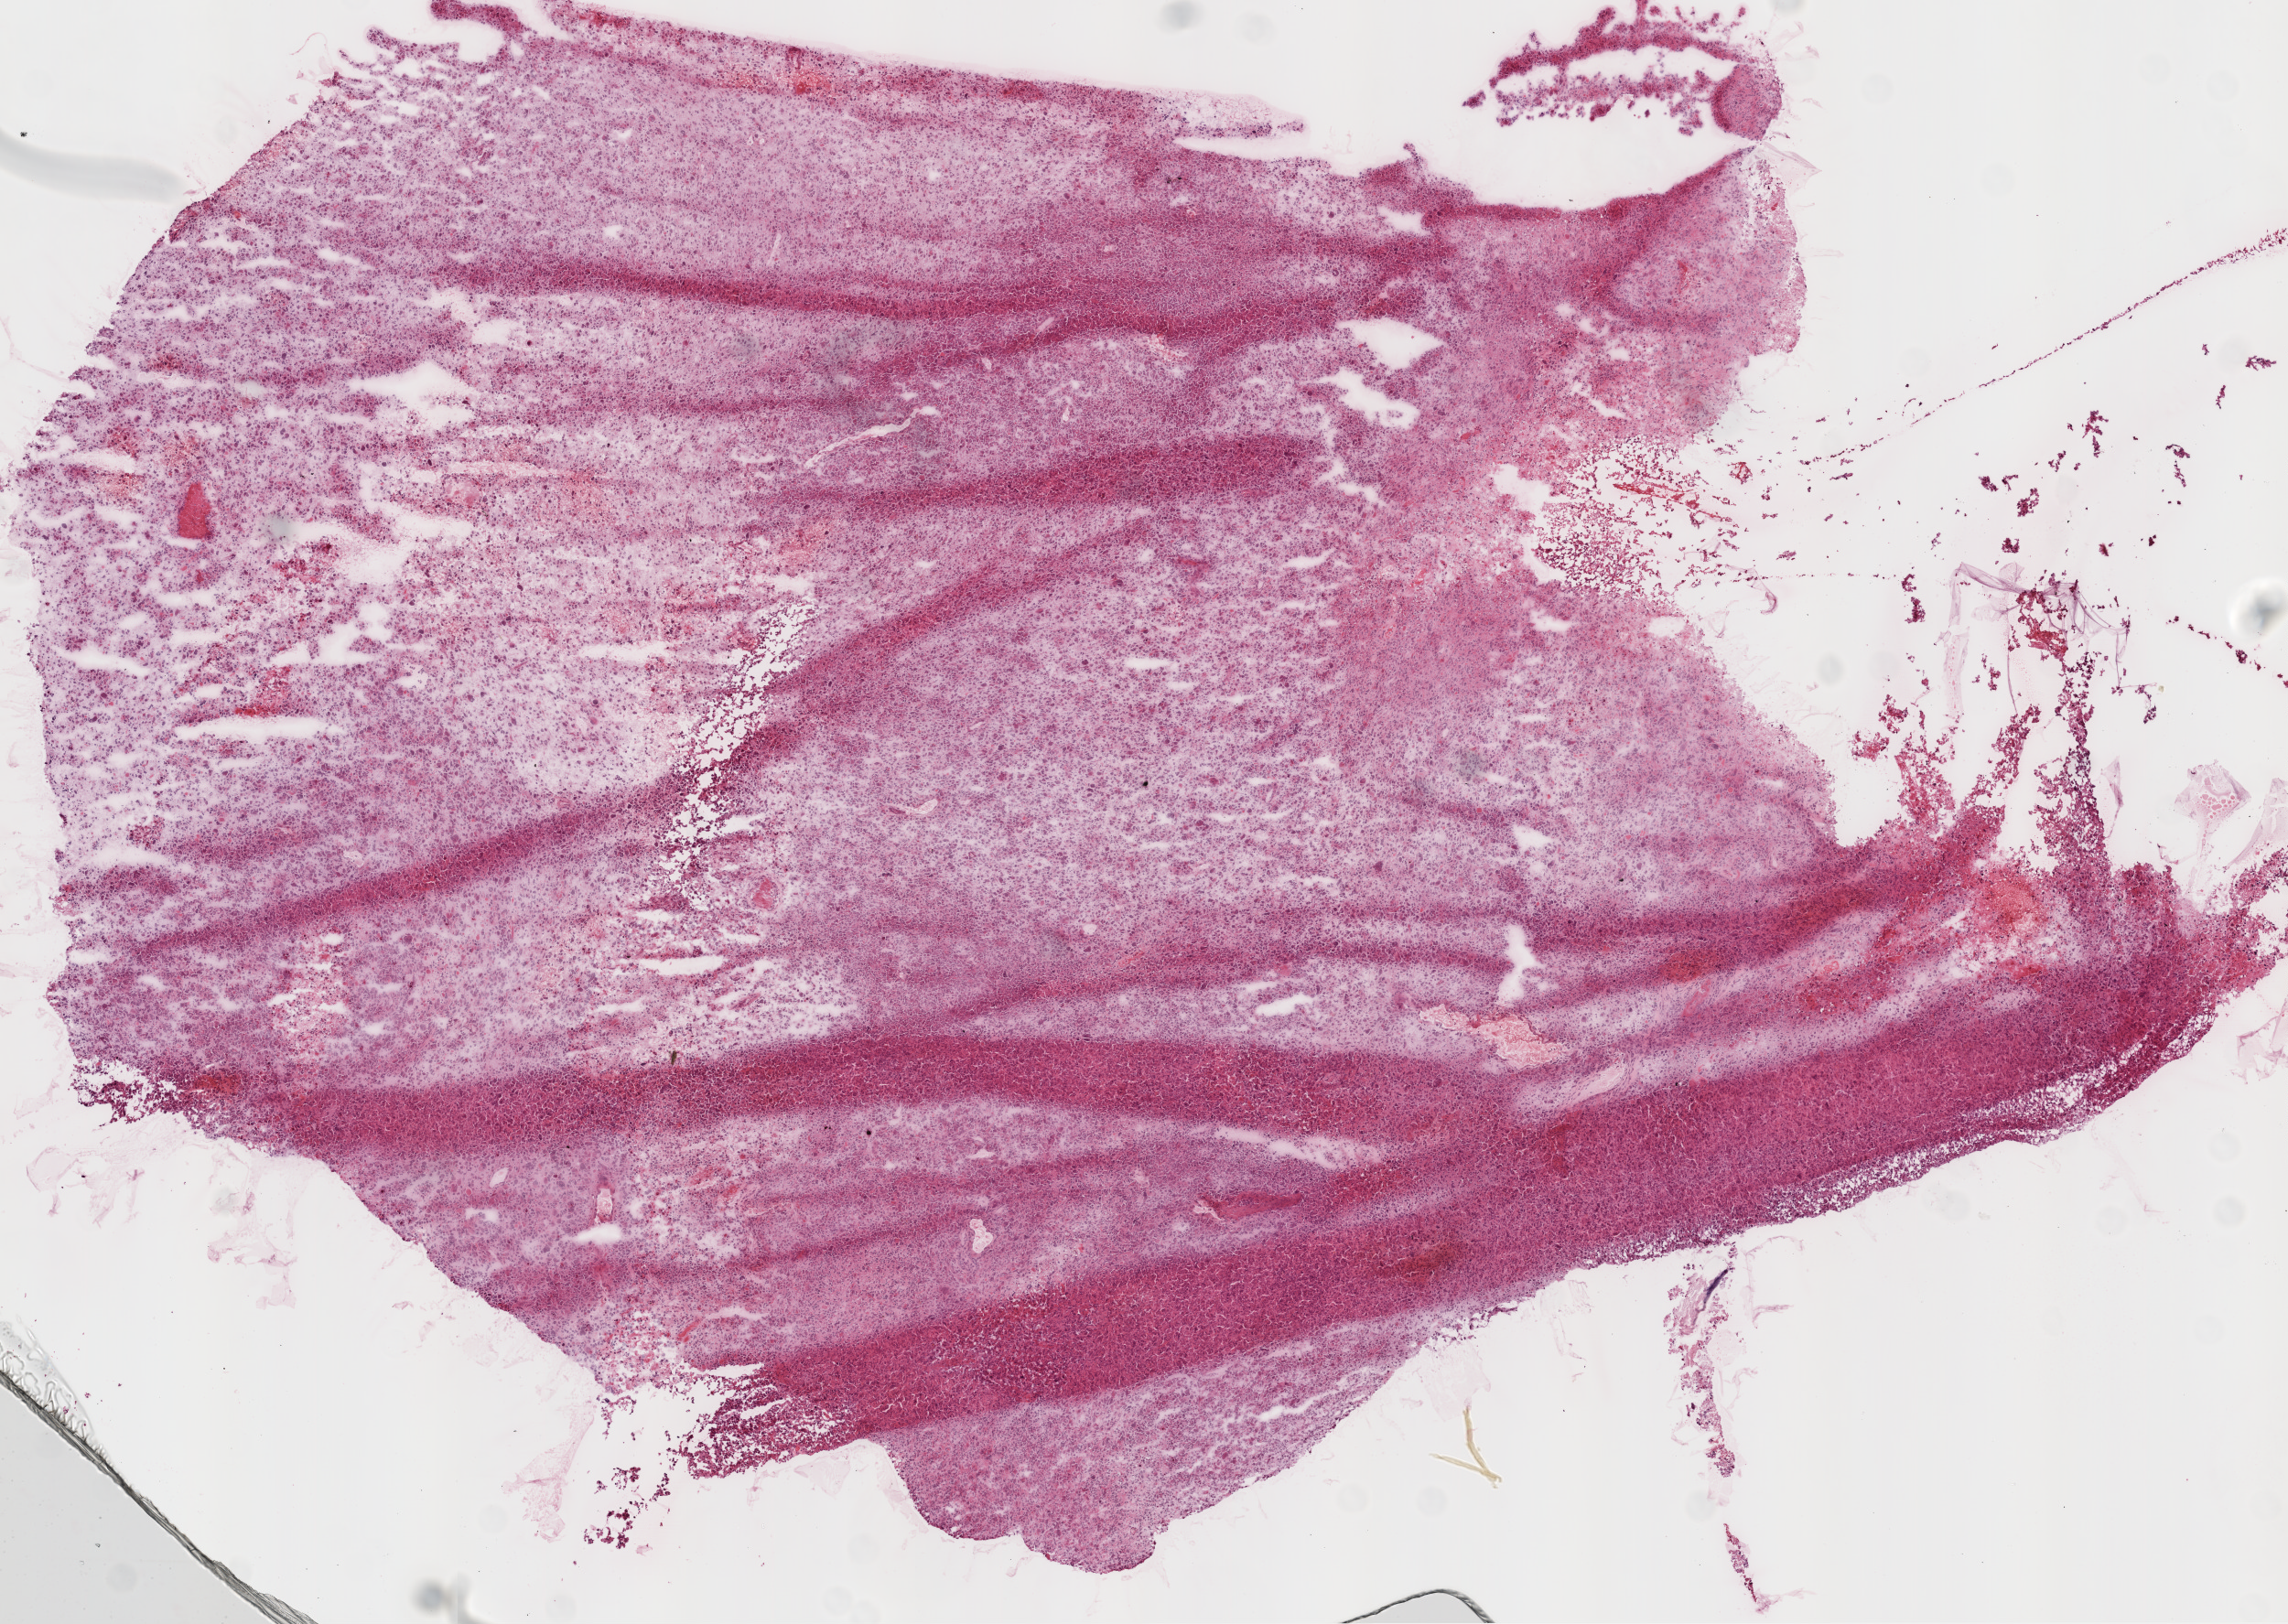
H&E-stained whole-slide image — shown as a low-resolution overview of the whole scanned area (about 10.0 x 7.1 mm, slide scanned at 20x); frozen section; primary tumour sample from the brain. Female, age 75 years at initial diagnosis. Pathologist review of this section (percent, as recorded): tumour cells 85%, tumour nuclei 95%, normal cells 0%, stromal cells 5%, necrosis 10%.
Pathologic diagnosis: Glioblastoma.